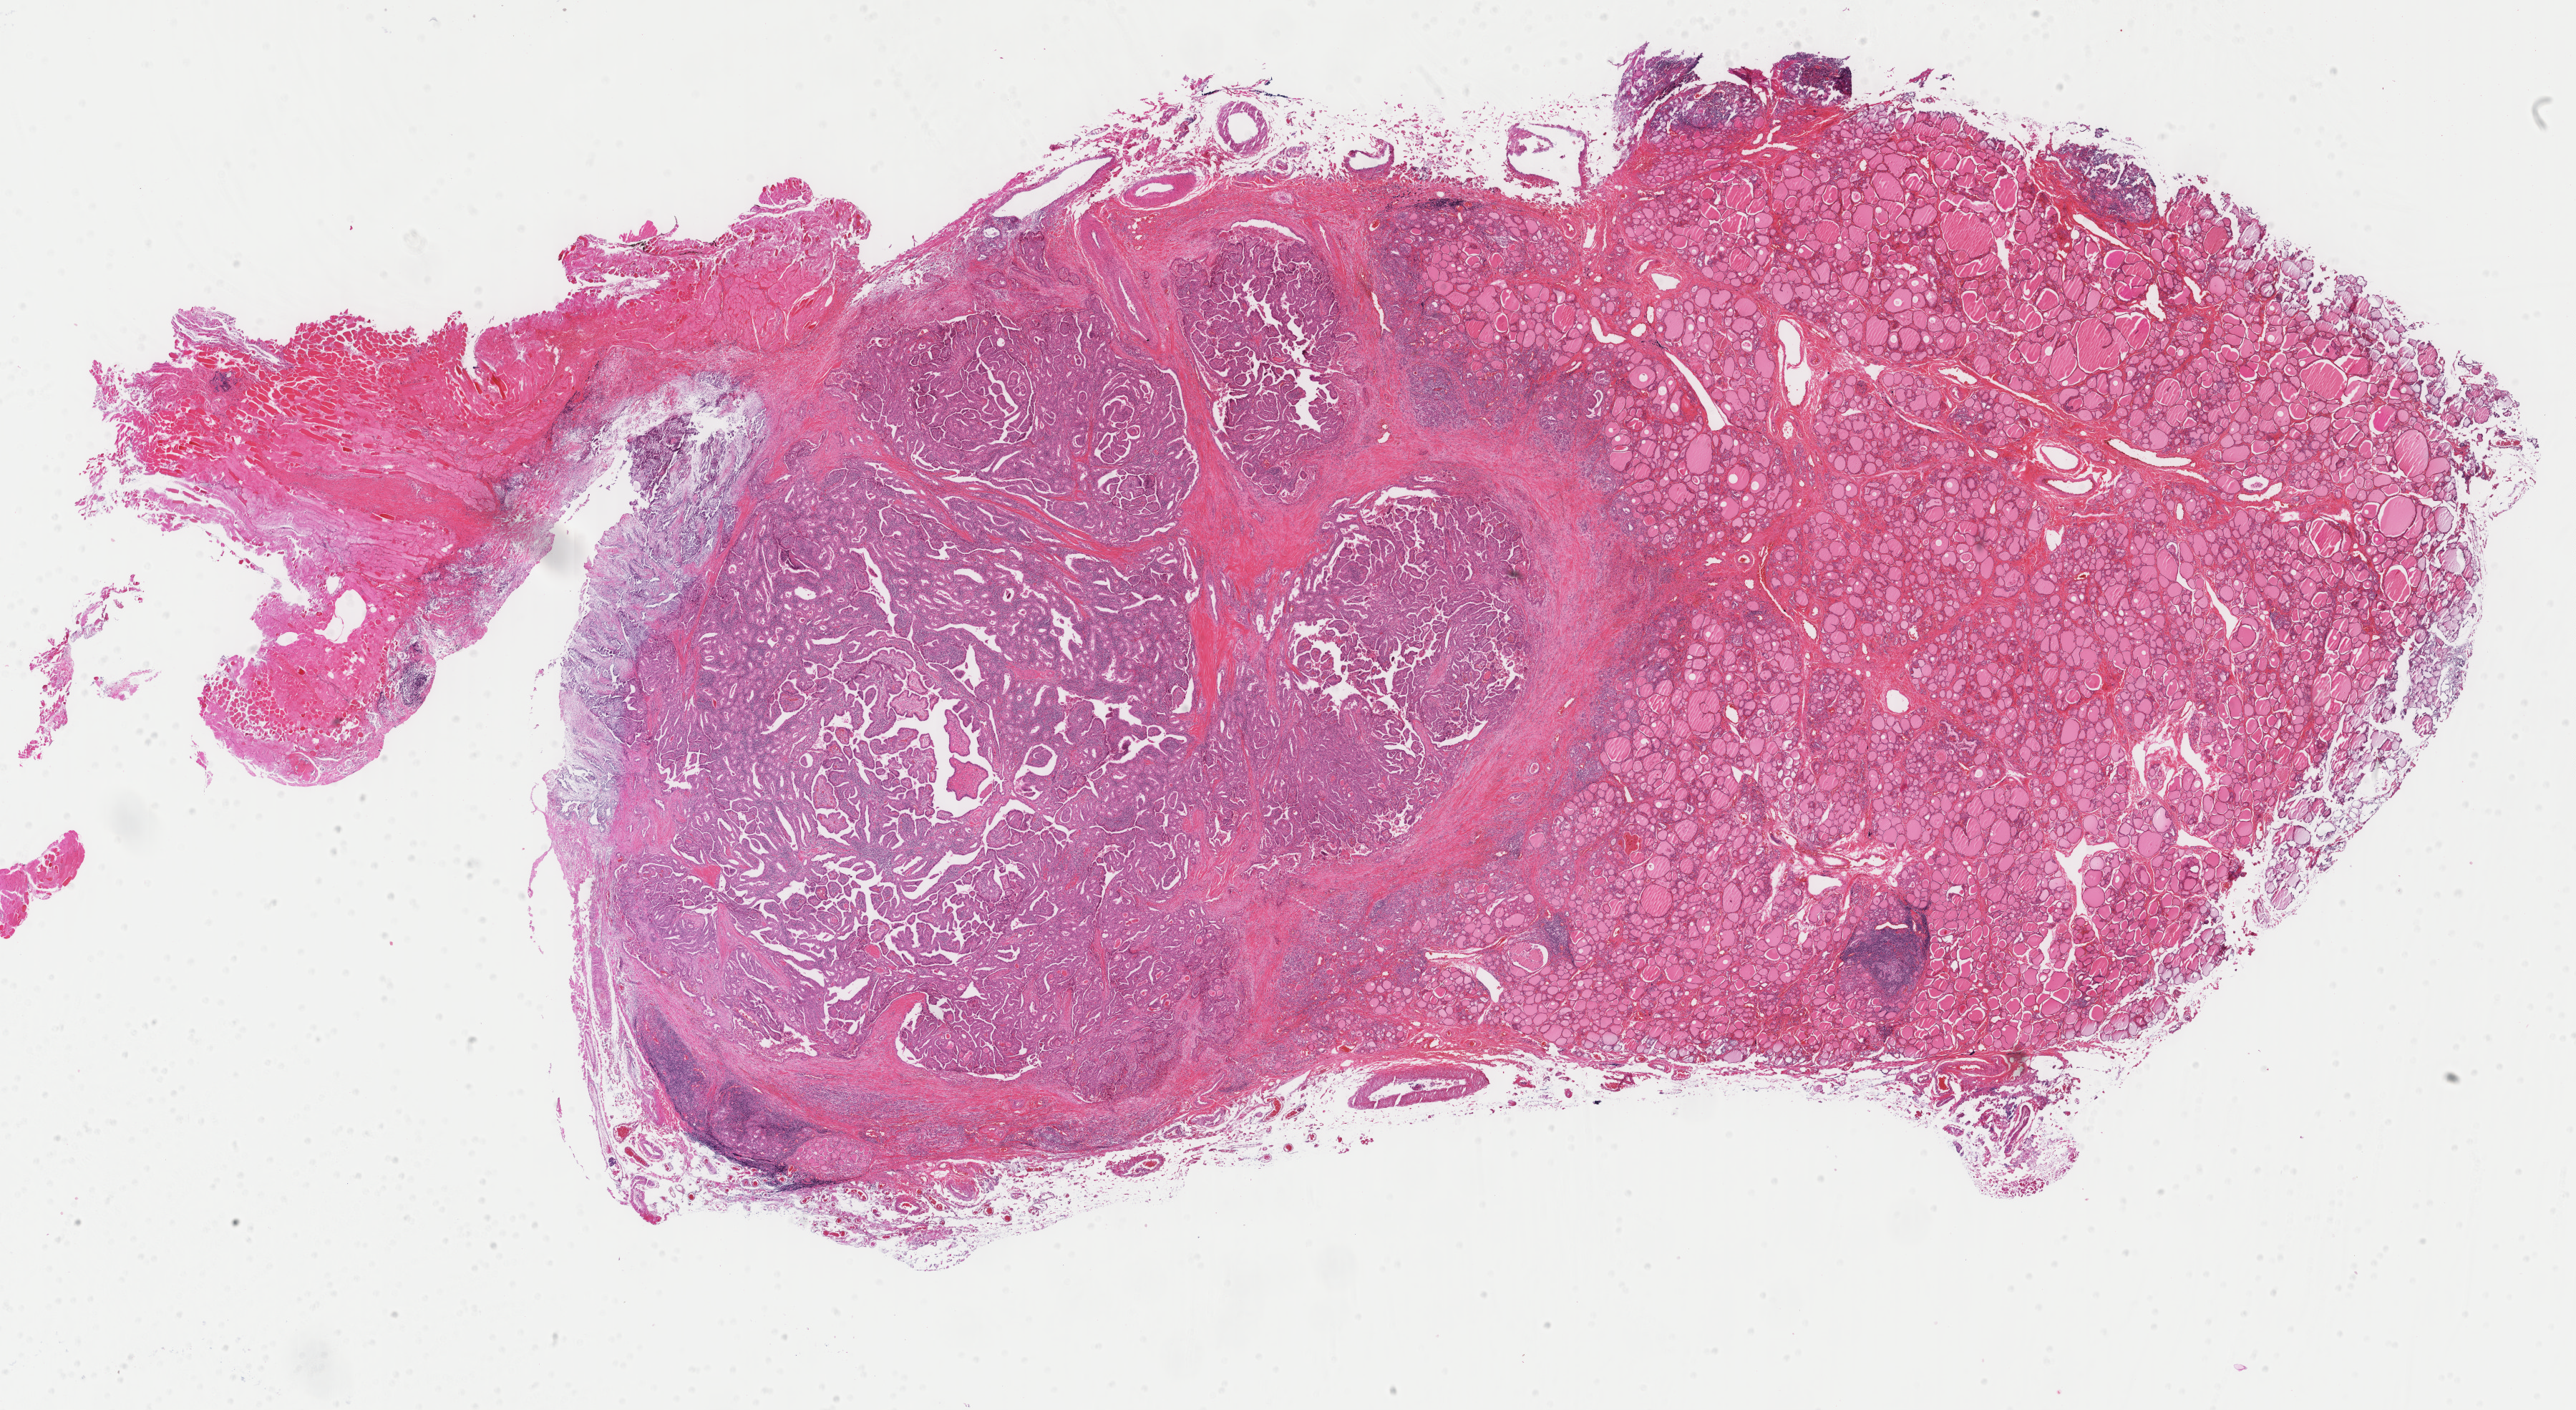
Whole-slide histology image, H&E, a low-resolution overview of the entire scanned area, about 28.6 x 15.6 mm (slide scanned at 40x); formalin-fixed paraffin-embedded (FFPE) diagnostic section; thyroid, primary tumour sample. Patient: female, age at initial diagnosis 47 years.
Lymph nodes positive (case pathology): 0 of 1 examined. Pathologic diagnosis: Papillary adenocarcinoma, NOS (thyroid gland). Laterality: left. AJCC pathologic stage: II (5th edition).